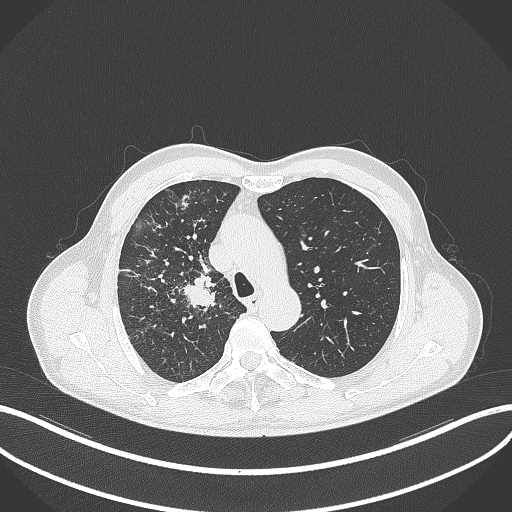
Chest CT, one axial slice. Position 353 of 490 along the scan axis. Reconstruction kernel B70f. 120 kVp. Lung window (W 1500 / L -600 HU). 1 mm slice thickness. 512 × 512 image matrix. Male patient, age 69 years. From the clinical record (not read from this slice): clinical TNM (as recorded): T2a N0 M0.
Structures marked on this image (bounding box drawn by a radiologist):
- lung tumour (recorded histology: adenocarcinoma): bounding box (x1, y1, x2, y2) in pixels: (183, 271, 219, 311)